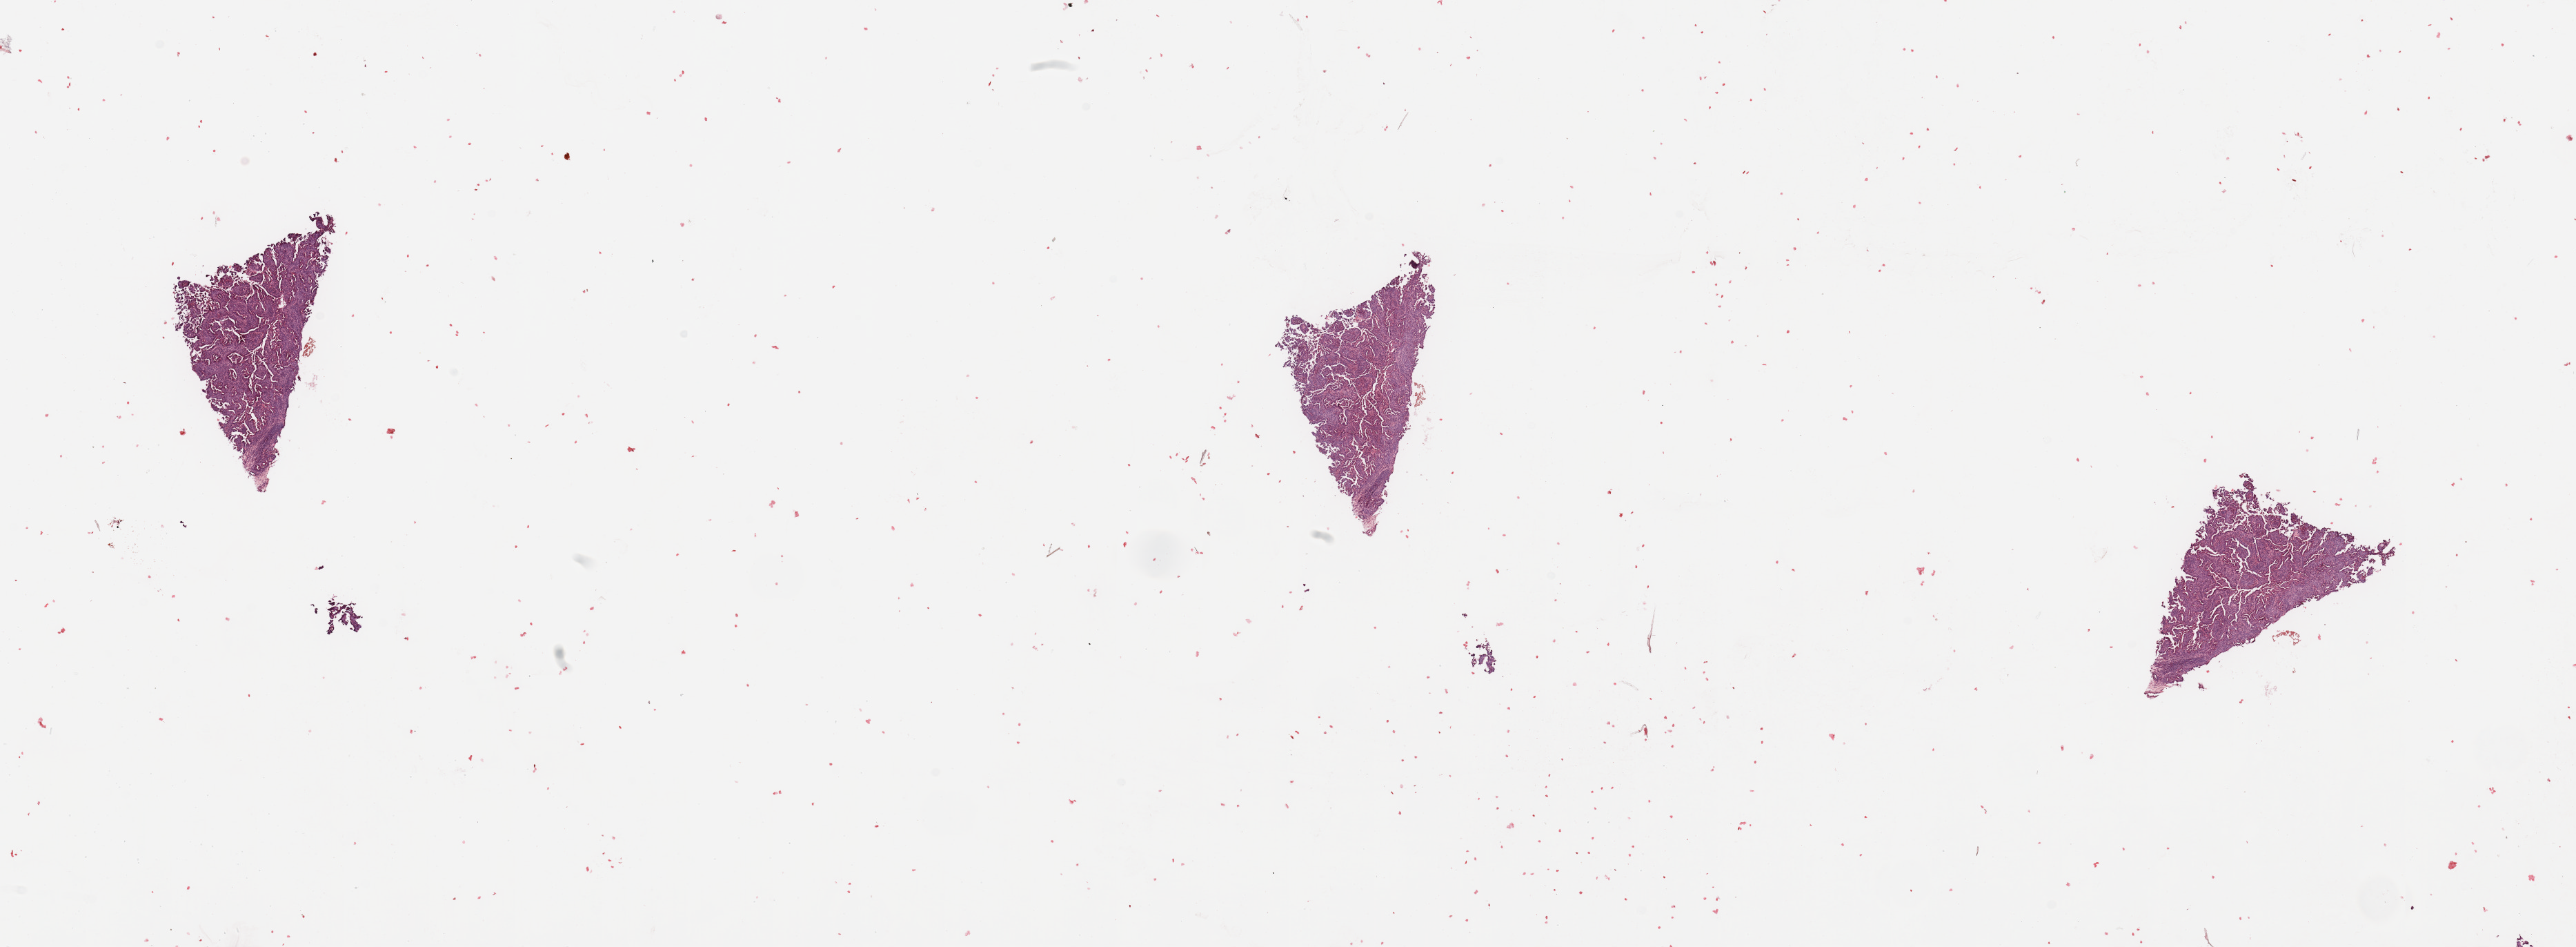
Hematoxylin and eosin (H&E) stained whole-slide image — whole scanned area (about 29.5 x 10.9 mm, acquisition: 20x scan) shown as a low-resolution overview, tumour tissue sample, sampled site: uterus. Patient: female, age 73 years. Histologic grade: G3 (poorly differentiated). Composition of this section per pathologist review: tumour nuclei 80%, necrosis 2%.
- AJCC pathologic stage: II
- histologic diagnosis: Endometrioid adenocarcinoma, NOS